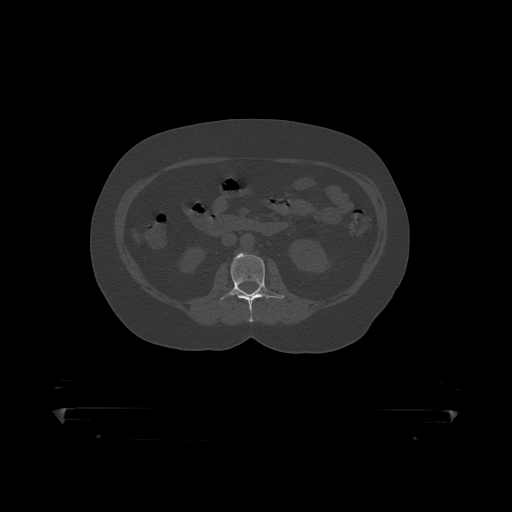
CT including the spine, one axial slice. Slice 116 of 390 in the series (ordered by position). Reconstruction kernel STANDARD. Bone window (W 1800 / L 400 HU). 1.25 mm slice thickness. 512 × 512 image matrix, field of view 650 × 650 mm. Male patient, age 60 years. From the clinical record (not read from this slice): primary cancer: prostate.
Structures marked on this image (semi-automatic segmentation, software-assisted and operator-edited):
- L2 vertebra: bounding box [x1, y1, x2, y2] px = [219, 253, 284, 319]